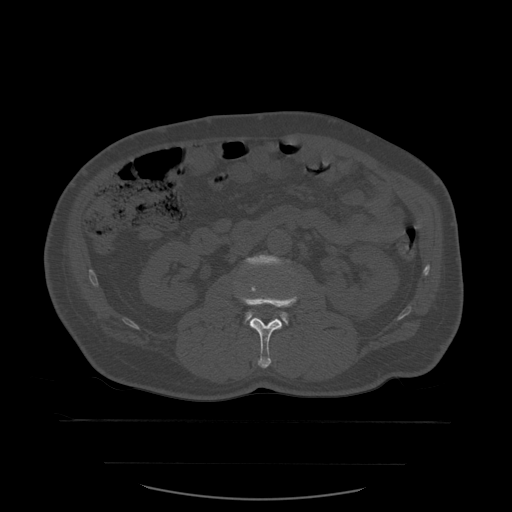
CT including the spine, one axial slice; slice 210 of 590 in the series (ordered by position); bone window (W 1800 / L 400 HU); 512 × 512 image matrix, field of view 479 × 479 mm. Patient age 71 years. From the clinical record (not read from this slice): primary cancer: lung.
Structures marked on this image (semi-automatic segmentation, software-assisted and operator-edited):
- L2 vertebra: bounding box (x1, y1, x2, y2) in pixels: (240, 286, 298, 369)
- L3 vertebra: (245, 255, 288, 323)